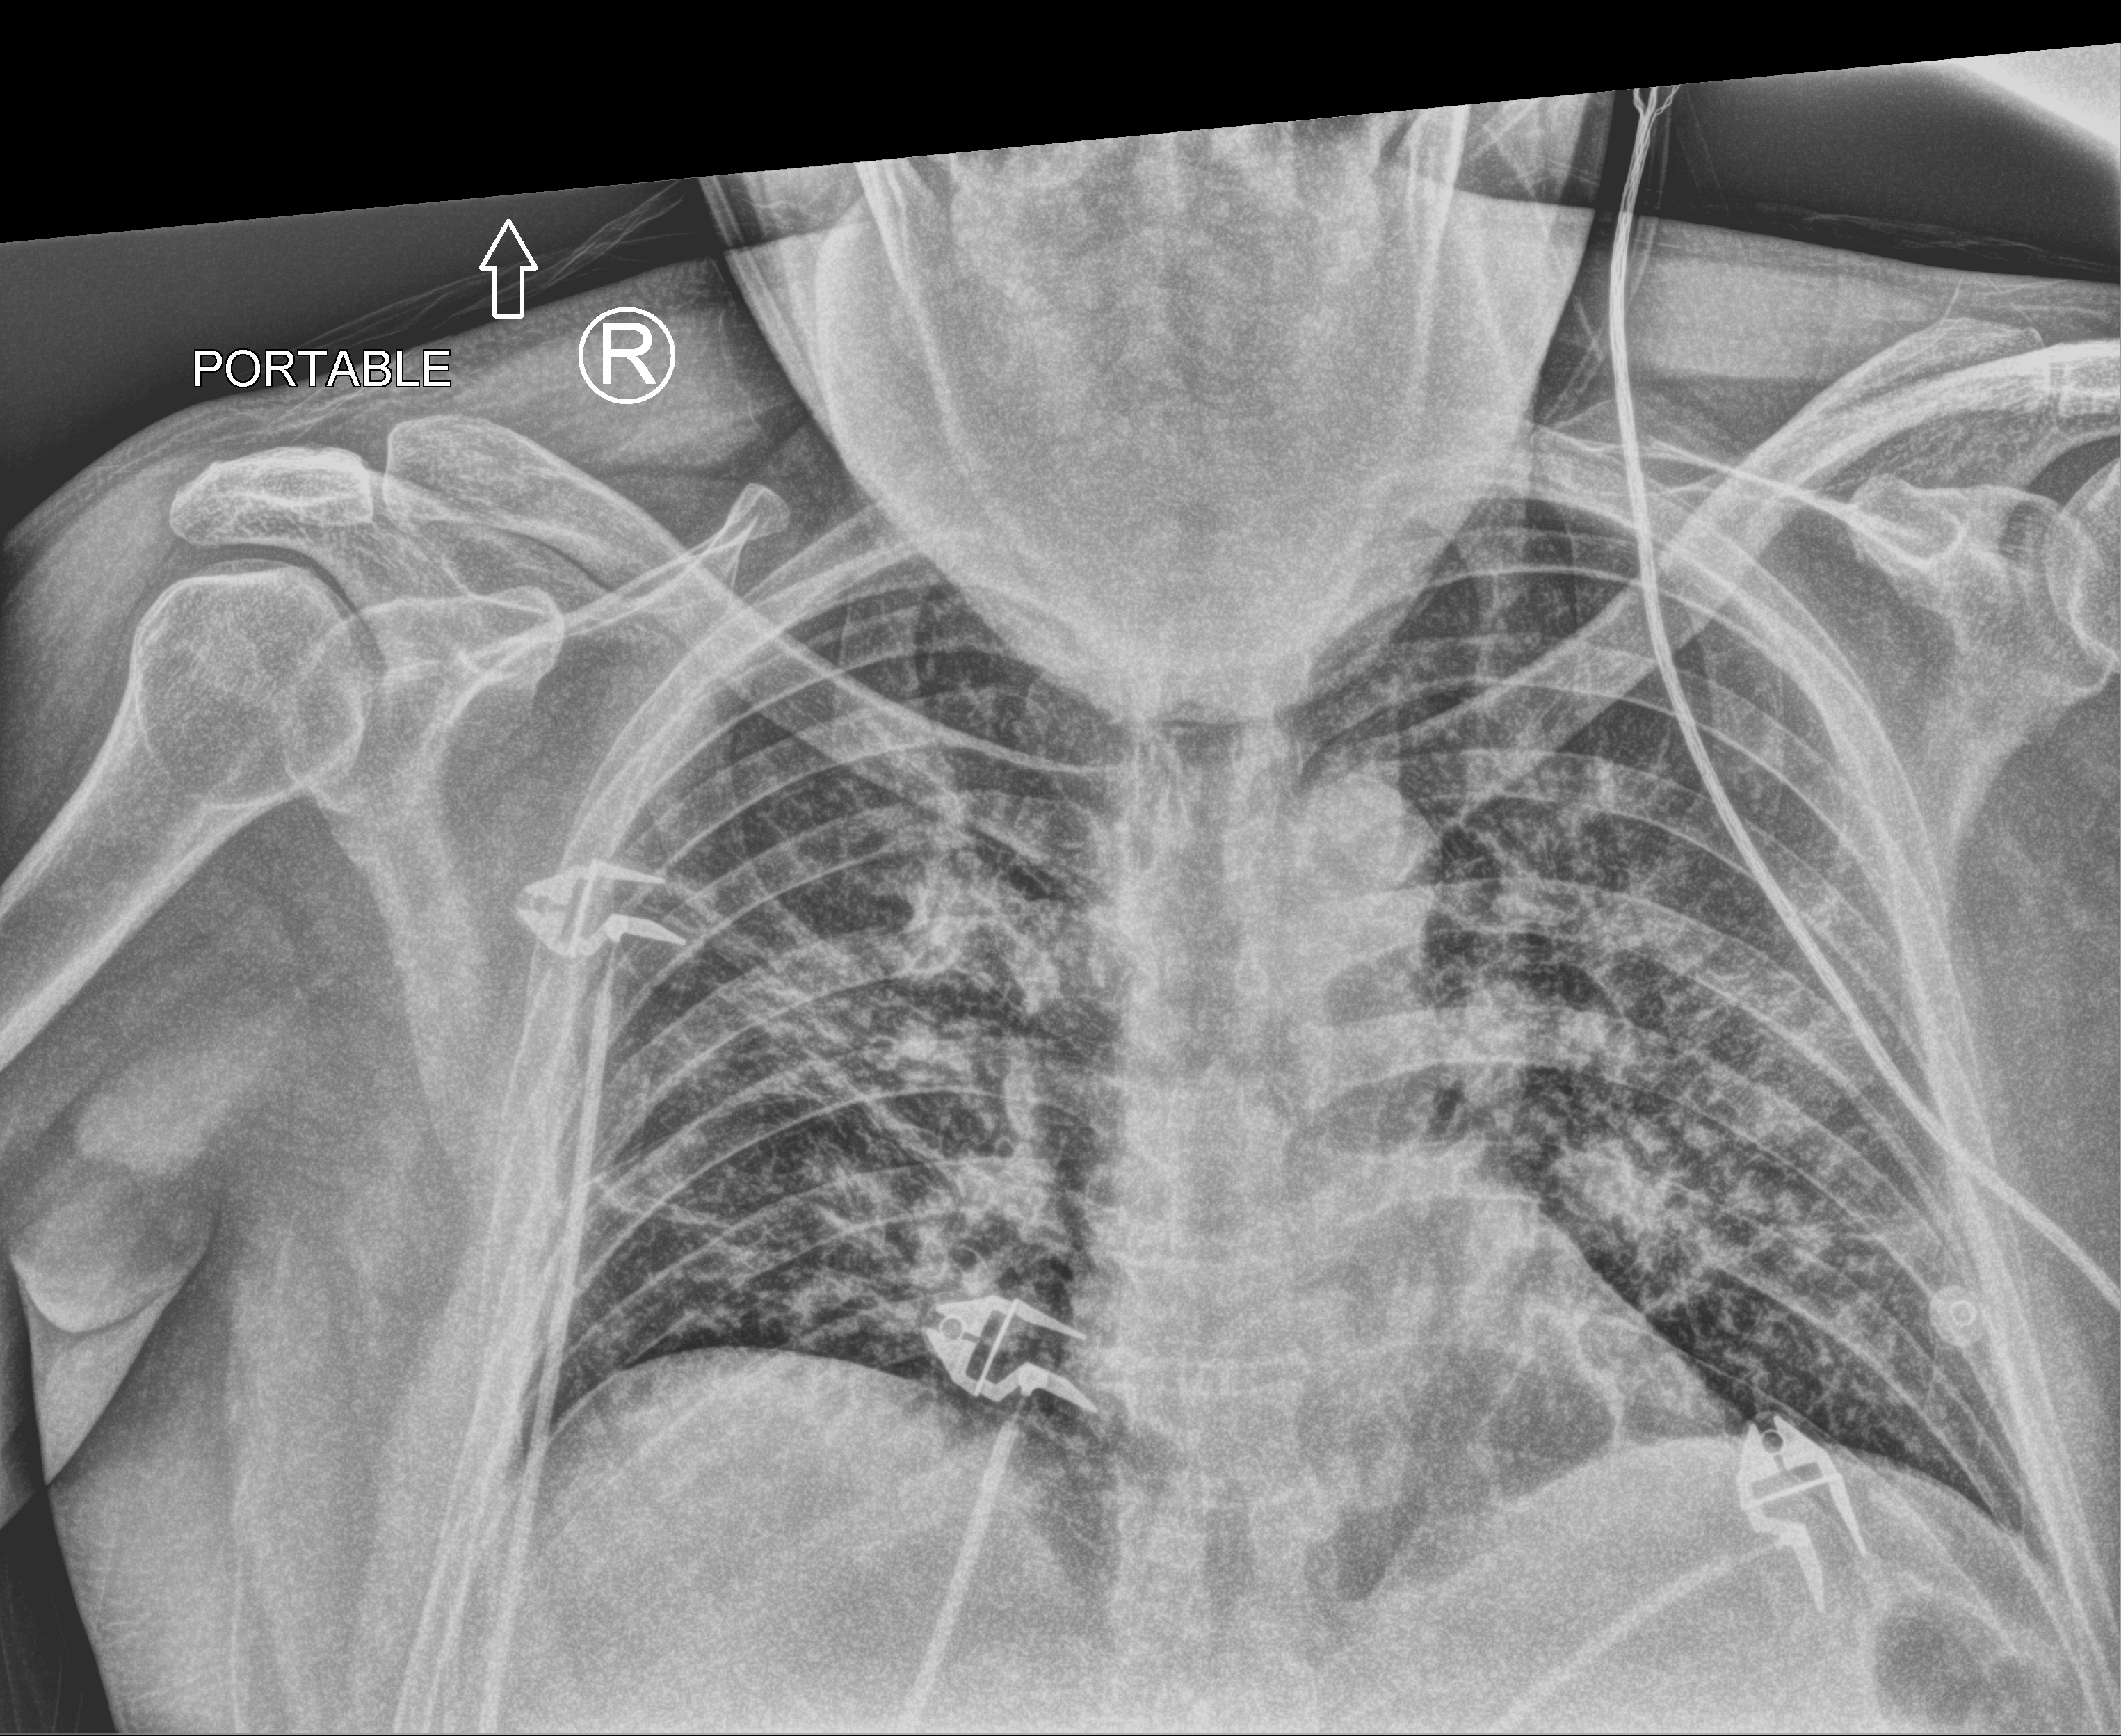
Portable chest radiograph. Patient hospitalised with COVID-19; male, aged 18–59 years.
From the hospital-stay record, not from the radiograph (when in the stay this image was taken is not recorded): hypertension (admission record): no; mechanically ventilated during this hospital stay: no; chronic kidney disease (admission record): no.